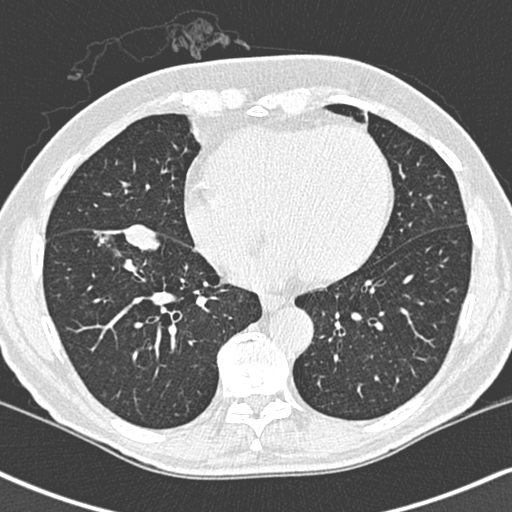
Low-dose screening chest CT, one axial slice; position 104 of 248 along the scan axis; lung window (W 1500 / L -600 HU); 1.3 mm slice thickness; 512 × 512 image matrix, field of view 323 × 323 mm.
Annotated regions visible in this slice (outlined manually by an expert reader):
- lesion 1 (tumor, lower lobe of right lung): bounding box <94,186,160,235> (left, top, right, bottom; pixels)